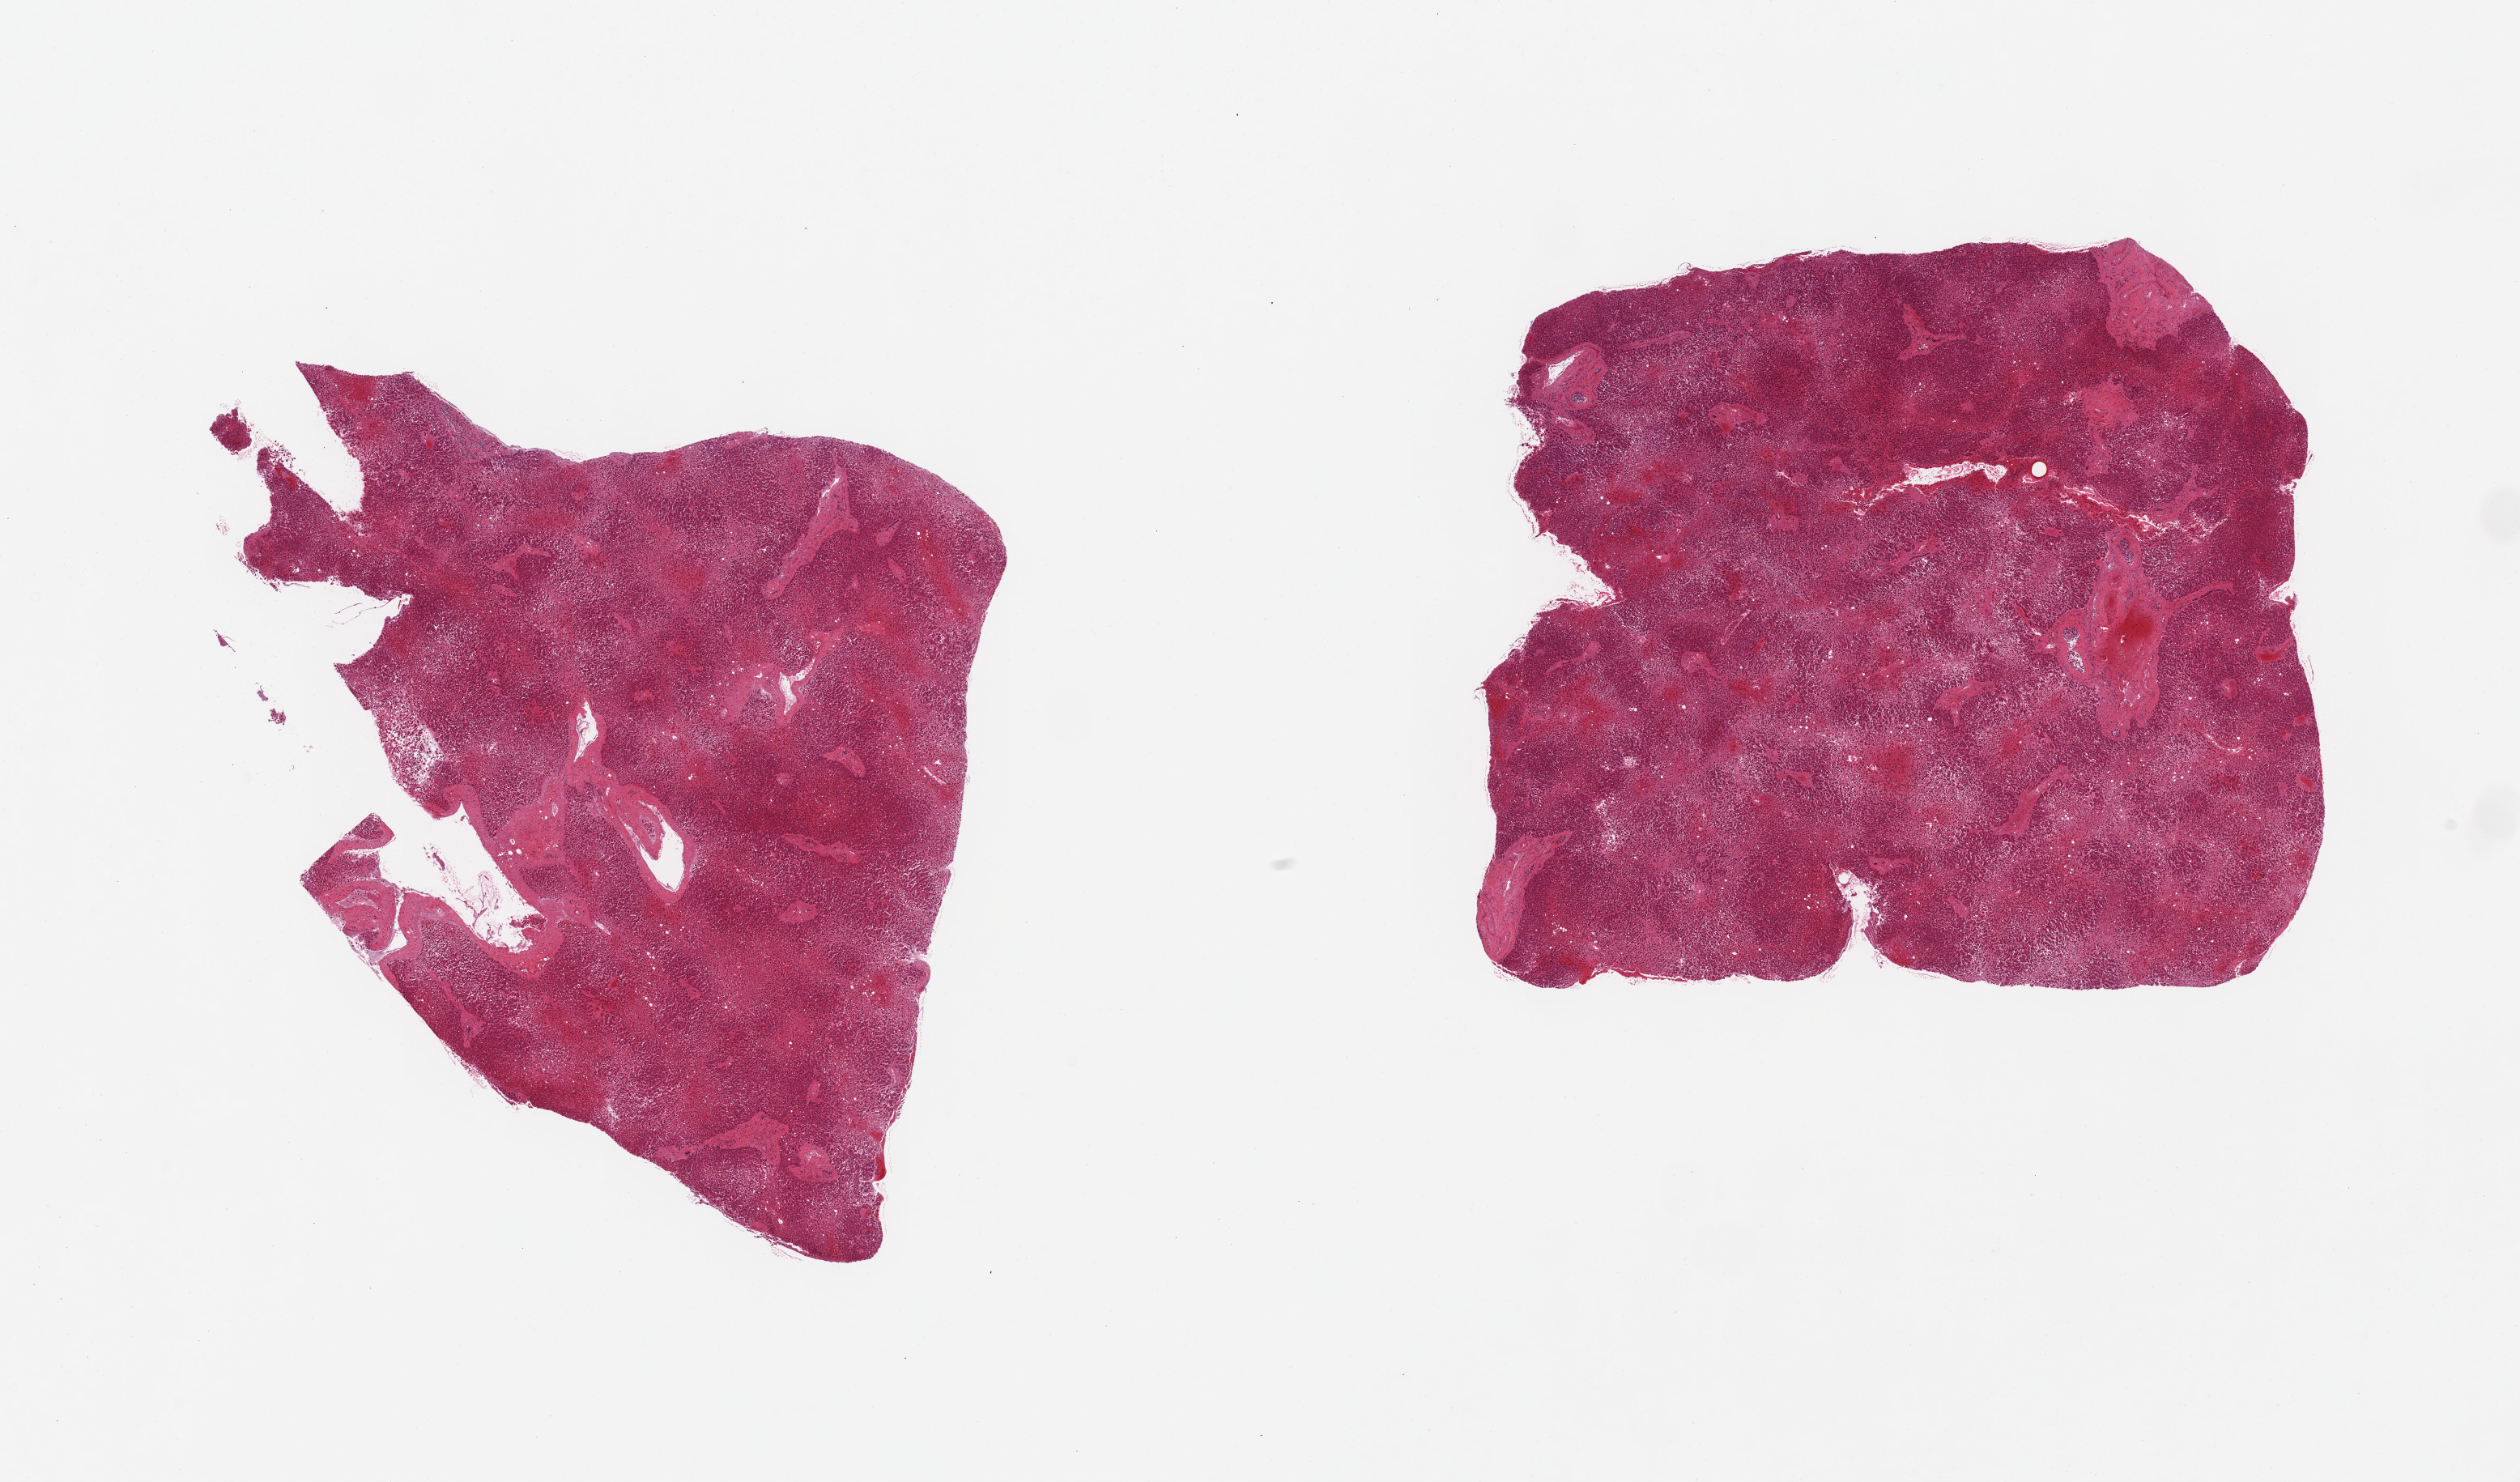
Digitized haematoxylin and eosin-stained section, low-resolution overview of the scanned area, about 24.6 x 14.5 mm (slide scanned at 20x). PAXgene-fixed paraffin-embedded (PFPE) section. Section of liver (target tissue). Tissue donor sample.
Reviewer comment on this tissue sample: 2 pieces; congested.